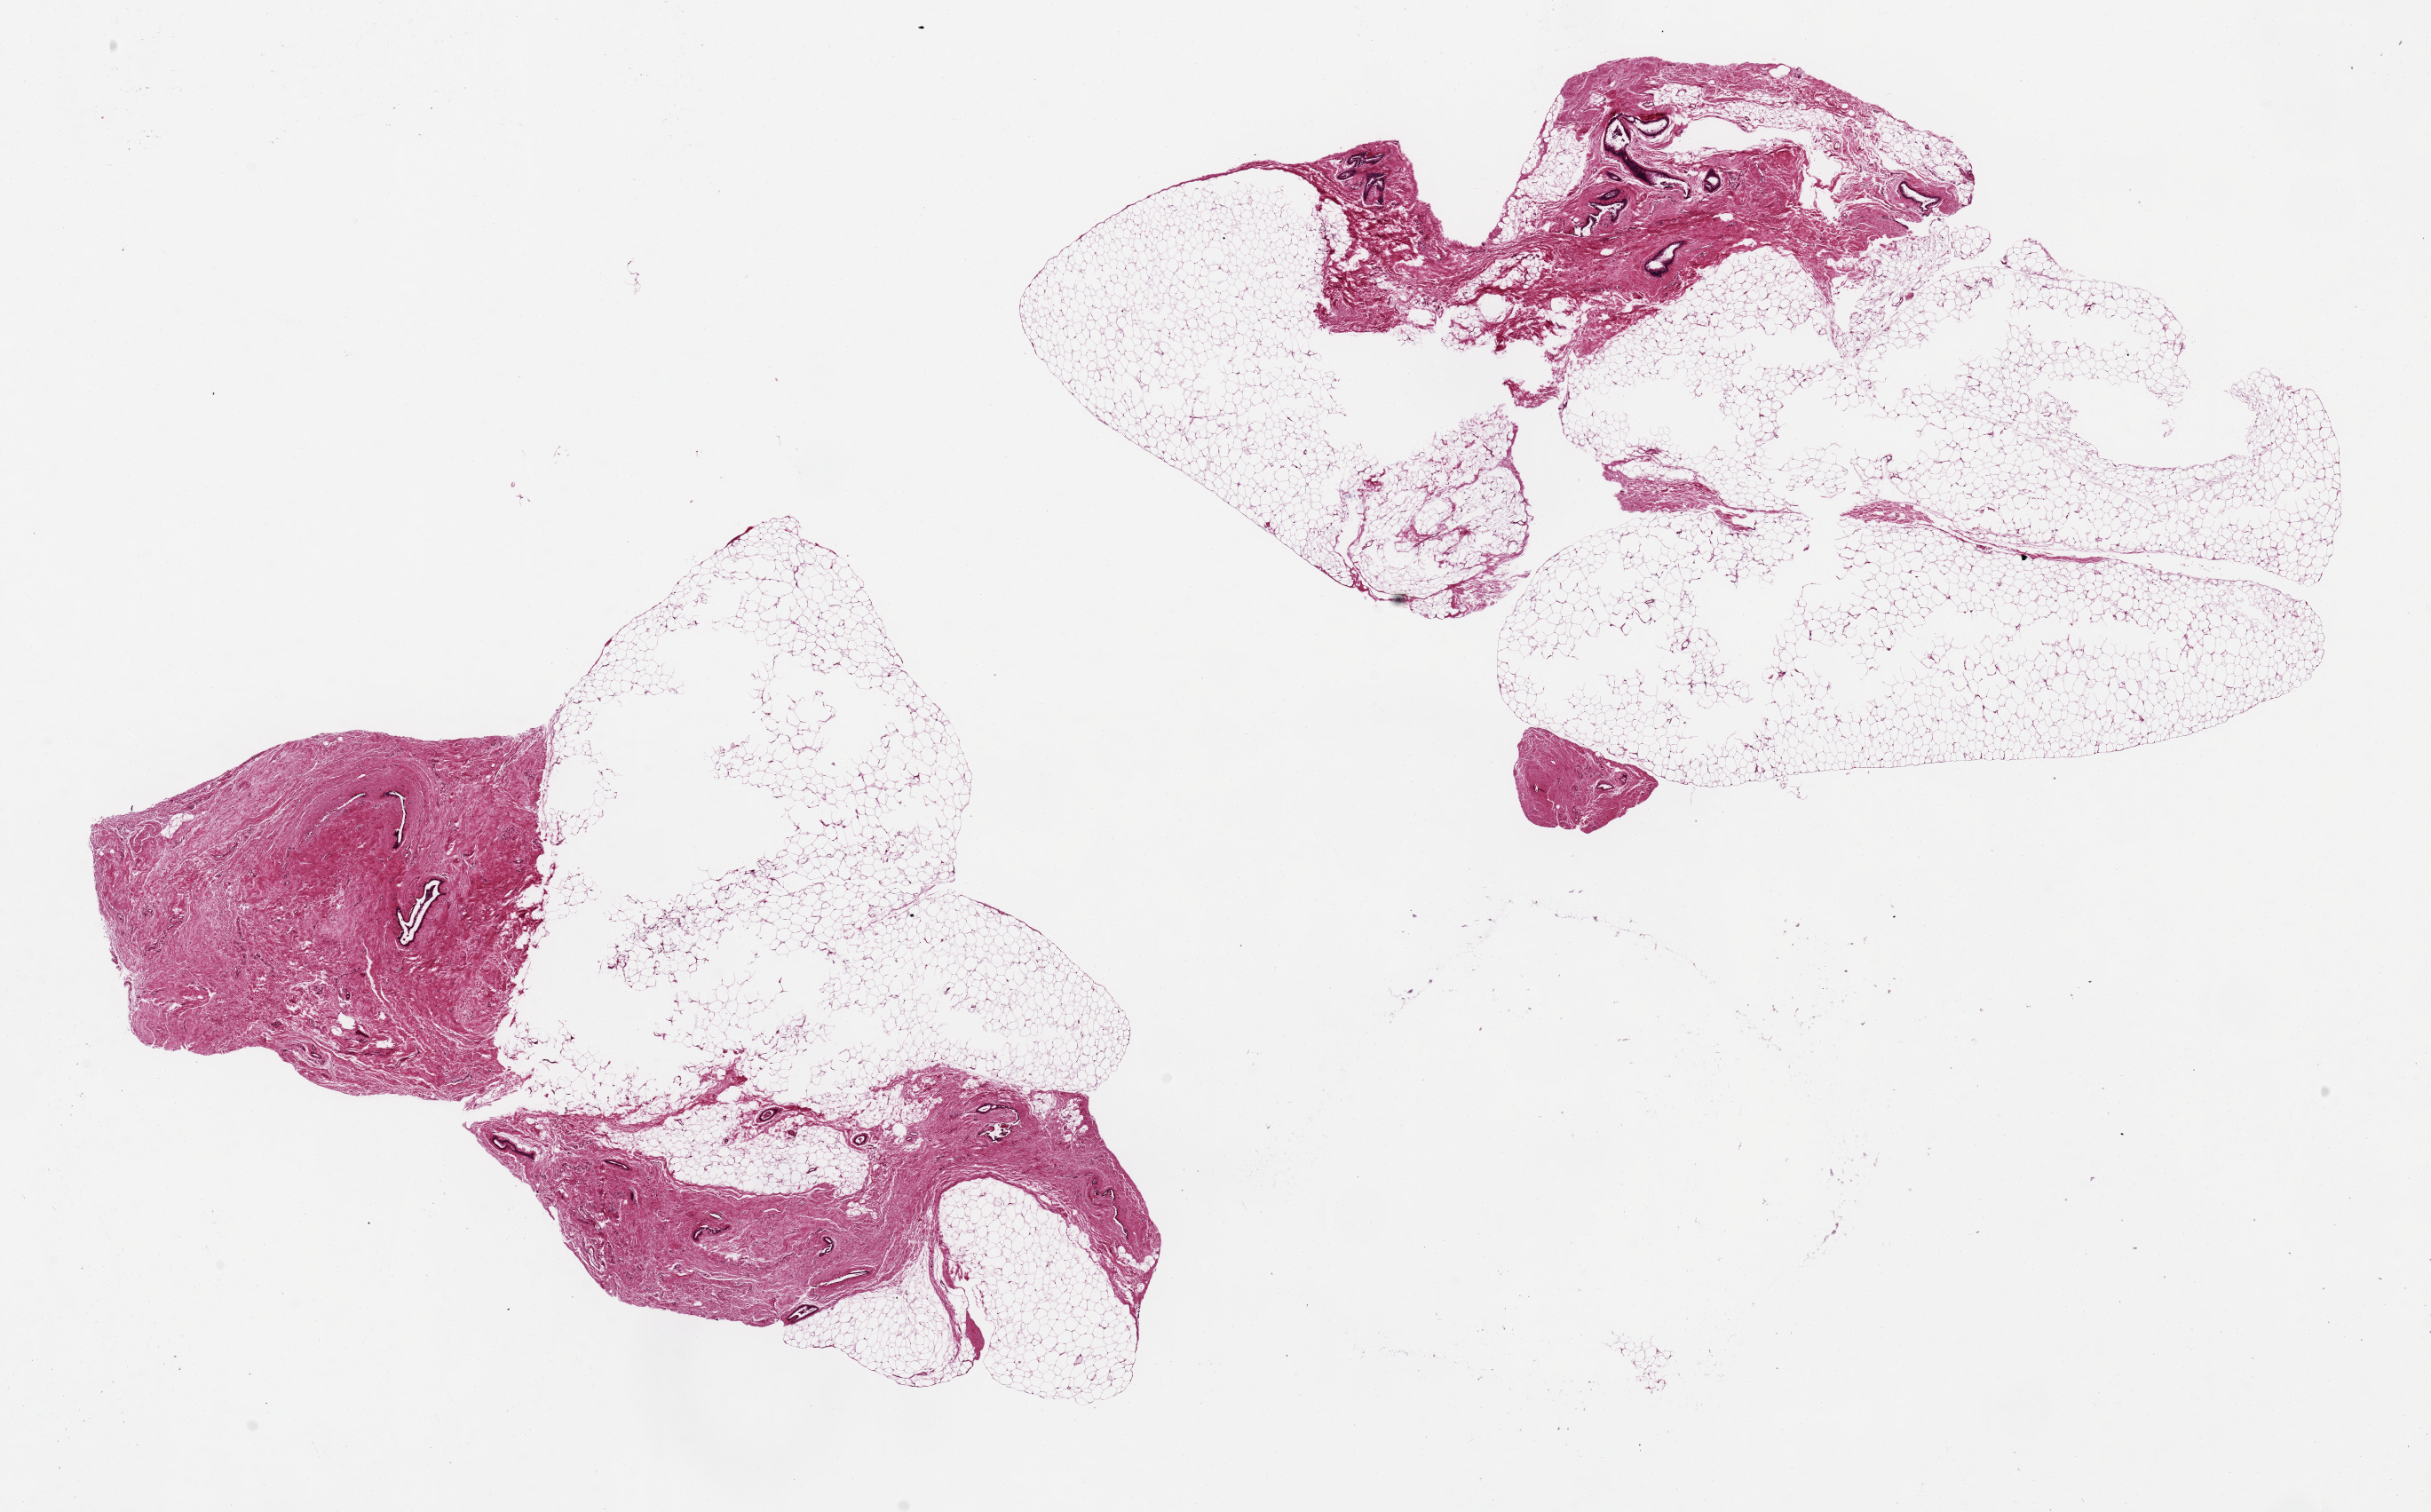
H&E whole-slide image — whole scanned area (about 21.7 x 13.5 mm, from a 20x scan) shown as a low-resolution overview; PAXgene-fixed paraffin-embedded (PFPE) section; target tissue: breast; tissue donor sample. Donor sex: male.
Pathologist's review note for this sample: 2 pieces, 7x7mm.